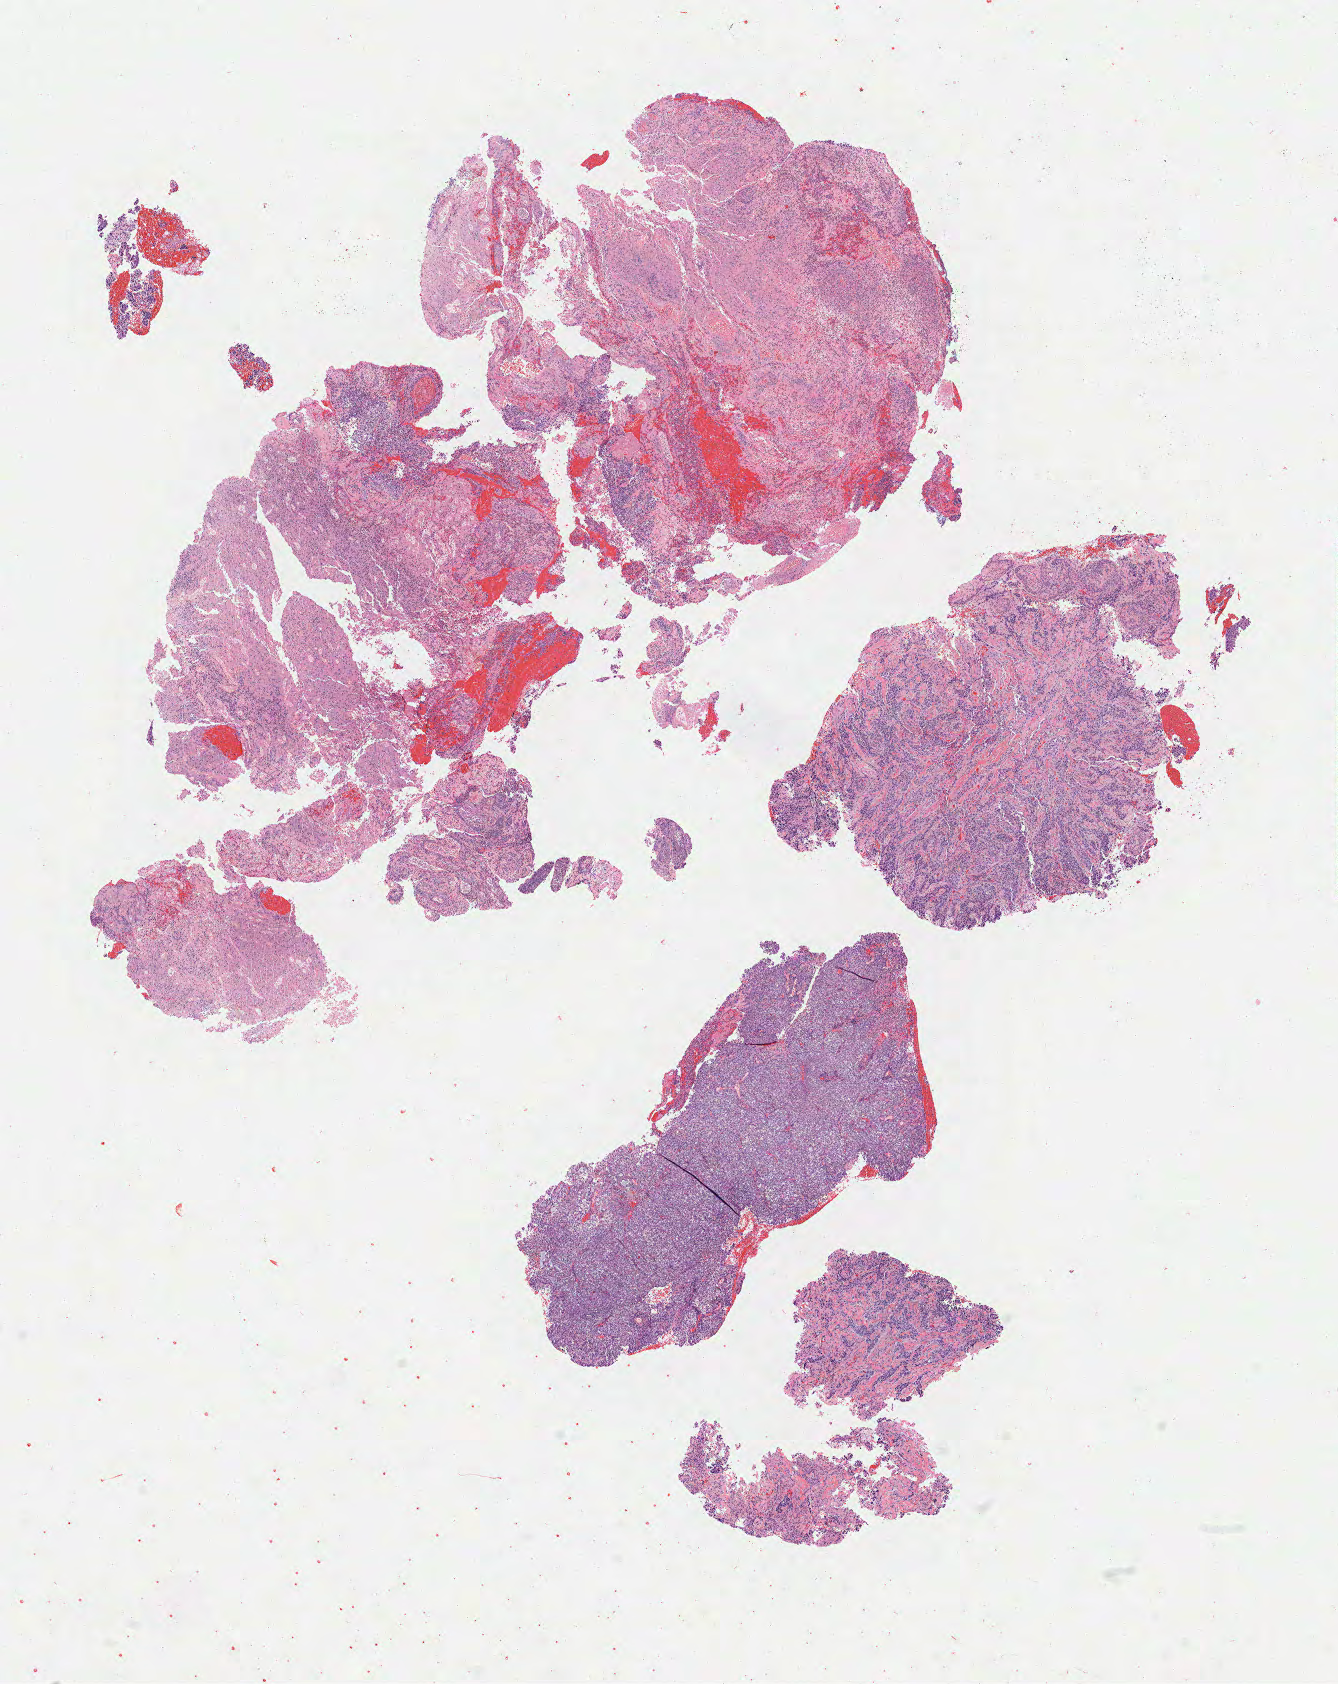
Whole-slide image, H&E stain, low-resolution overview of the scanned area, about 10.7 x 13.4 mm. Tumor tissue. Anatomic site: cervix. Female patient, aged 63.
Diagnosis: Squamous cell carcinoma, large cell, nonkeratinizing, NOS.